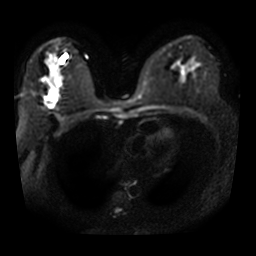
Breast MRI, one axial slice; diffusion-weighted series; image 2 of 4 stored at this slice position (different b-values; order by instance number); 3 T; 256 × 256 image matrix. Female patient.
Annotated regions visible in this slice (manually delineated by an expert):
- tumour on diffusion-weighted imaging: bounding box (x1, y1, x2, y2) in pixels: (45, 92, 57, 108)